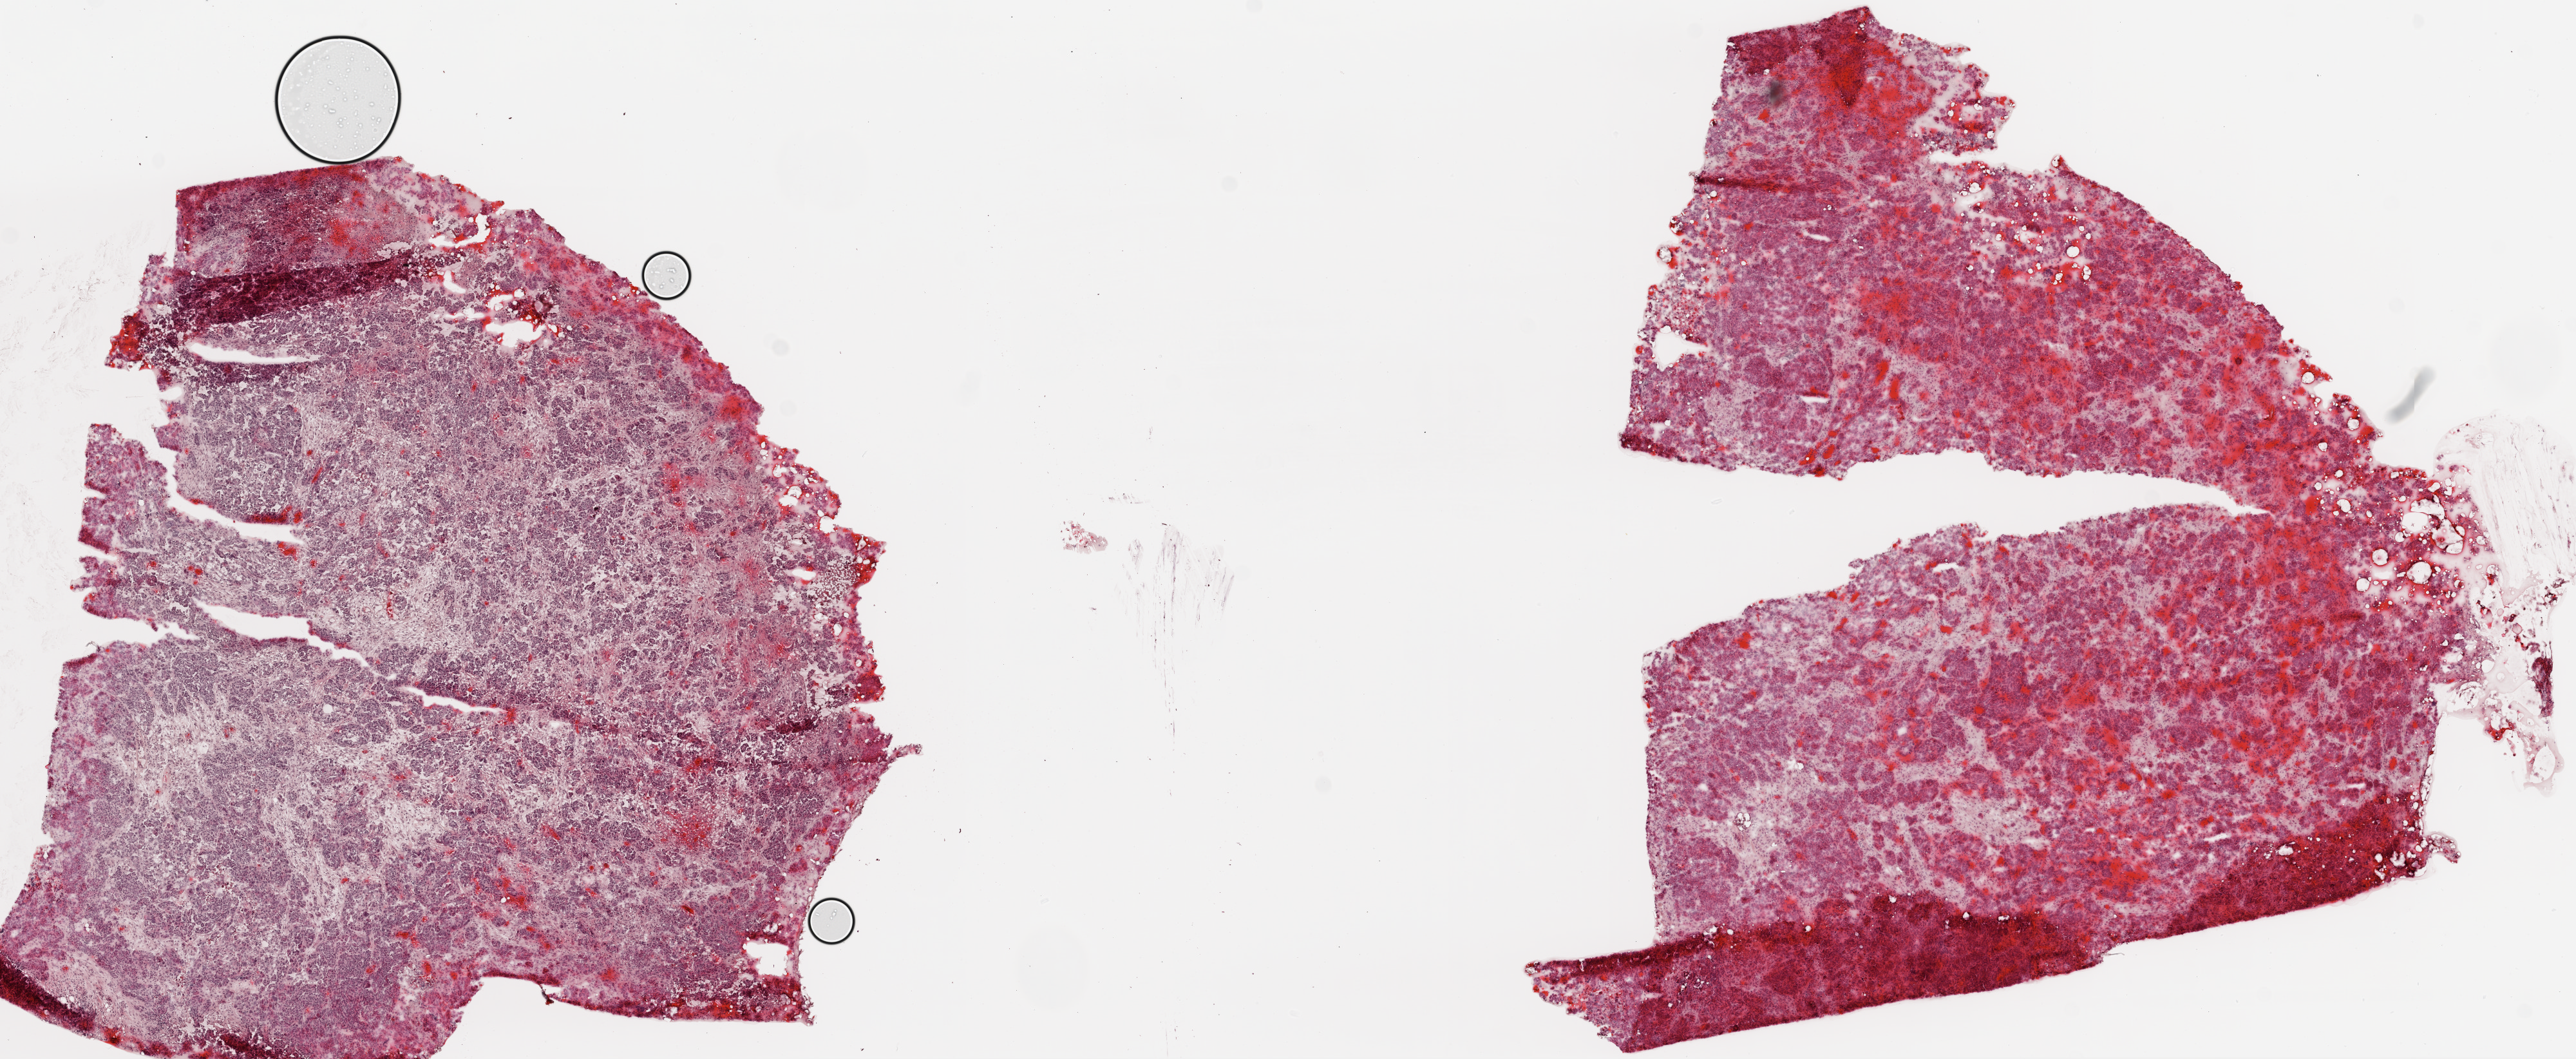
Whole-slide histology image, H&E-stained, low-resolution overview of the scanned area, about 16.0 x 6.6 mm (slide scanned at 20x); frozen section from the top of the tissue portion; sample: primary tumour, ovary. Patient: female, age at initial diagnosis 68 years. Histologic grade: G3 (poorly differentiated). Slide review estimates, as recorded: tumour cells 75%, tumour nuclei 70%, normal cells 20%, stromal cells 0%, necrosis 5%.
- FIGO stage: IIIC
- pathologic diagnosis: Serous cystadenocarcinoma, NOS